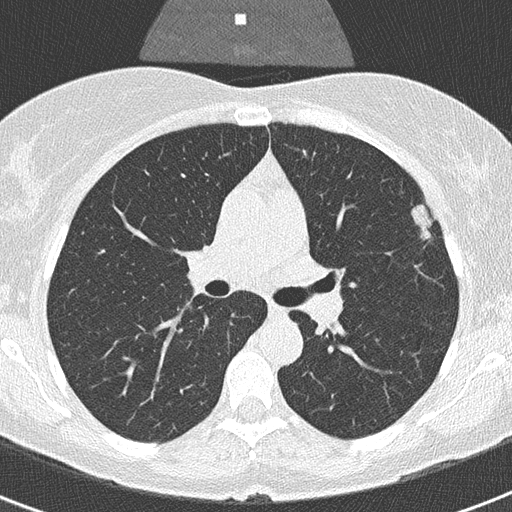
Low-dose screening chest CT, axial slice, second screening round (one year after baseline), lung window (W 1500 / L -600 HU), 120 kVp, slice 116 of 320 in the series. Female participant, aged 56 years at enrolment. Former smoker at enrolment.
Expert-annotated lung lesion, box from (x=406, y=201) to (x=454, y=254) px. Reader record for this screening exam (exam-level; its link to the box is not recorded): non-calcified nodule or mass ≥4 mm, left upper lobe, 20 × 9 mm, smooth margins, soft tissue attenuation, pre-existing on the prior screen: yes; interval growth: yes. Official screen result: positive, other. Later outcome: lung cancer diagnosed 55 days after this screen — adenocarcinoma, NOS, left upper lobe, moderately differentiated (G2), stage IA (AJCC 6th edition), 11 mm at pathology.